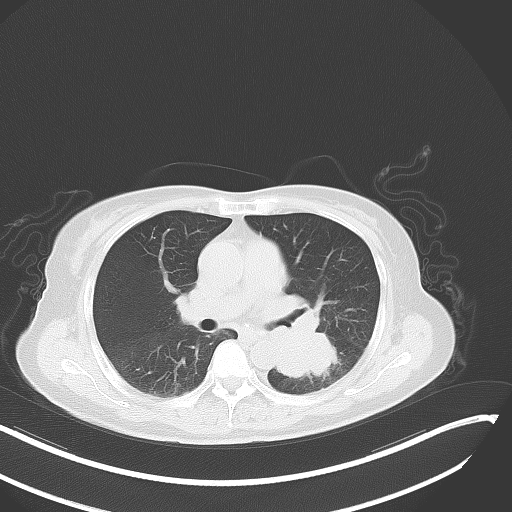
Chest CT, one axial slice. Slice 22 of 48 in the series (ordered by position). Reconstruction kernel B70f. Lung window (W 1500 / L -600 HU). 512 × 512 image matrix. Patient: female, 64 years. From the clinical record (not read from this slice): clinical TNM (as recorded): T3 N1 M1.
Annotated regions visible in this slice (bounding box drawn by a radiologist):
- lung tumour (recorded histology: small cell carcinoma): bounding box [x1, y1, x2, y2] px = [271, 325, 343, 383]